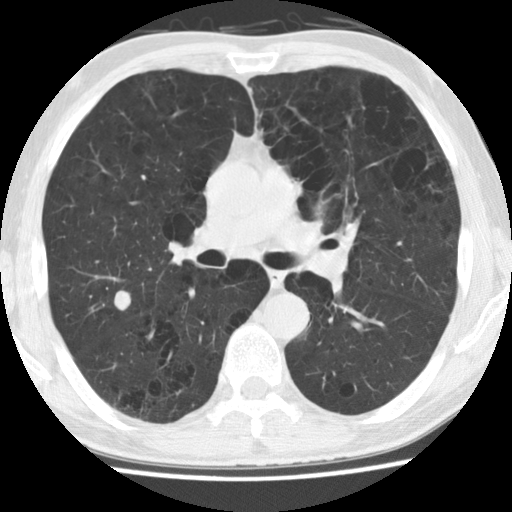
Axial slice from a low-dose chest CT screening exam, baseline annual screen, lung window (W 1500 / L -600 HU), 2.5 mm slice thickness, 512 × 512 image matrix. Male participant, aged 62 years at enrolment. Current smoker at enrolment.
- Expert reader's lesion annotation, bounding box [x1, y1, x2, y2] px = [89, 266, 148, 328].
- The screening reader recorded 2 non-calcified nodules or masses ≥4 mm on this exam; which of them this box marks is not recorded.
- Participant outcome: lung cancer diagnosed 288 days after this screen — oat cell carcinoma, right upper lobe, undifferentiated (G4), stage IV (AJCC 6th edition), 30 mm at pathology.